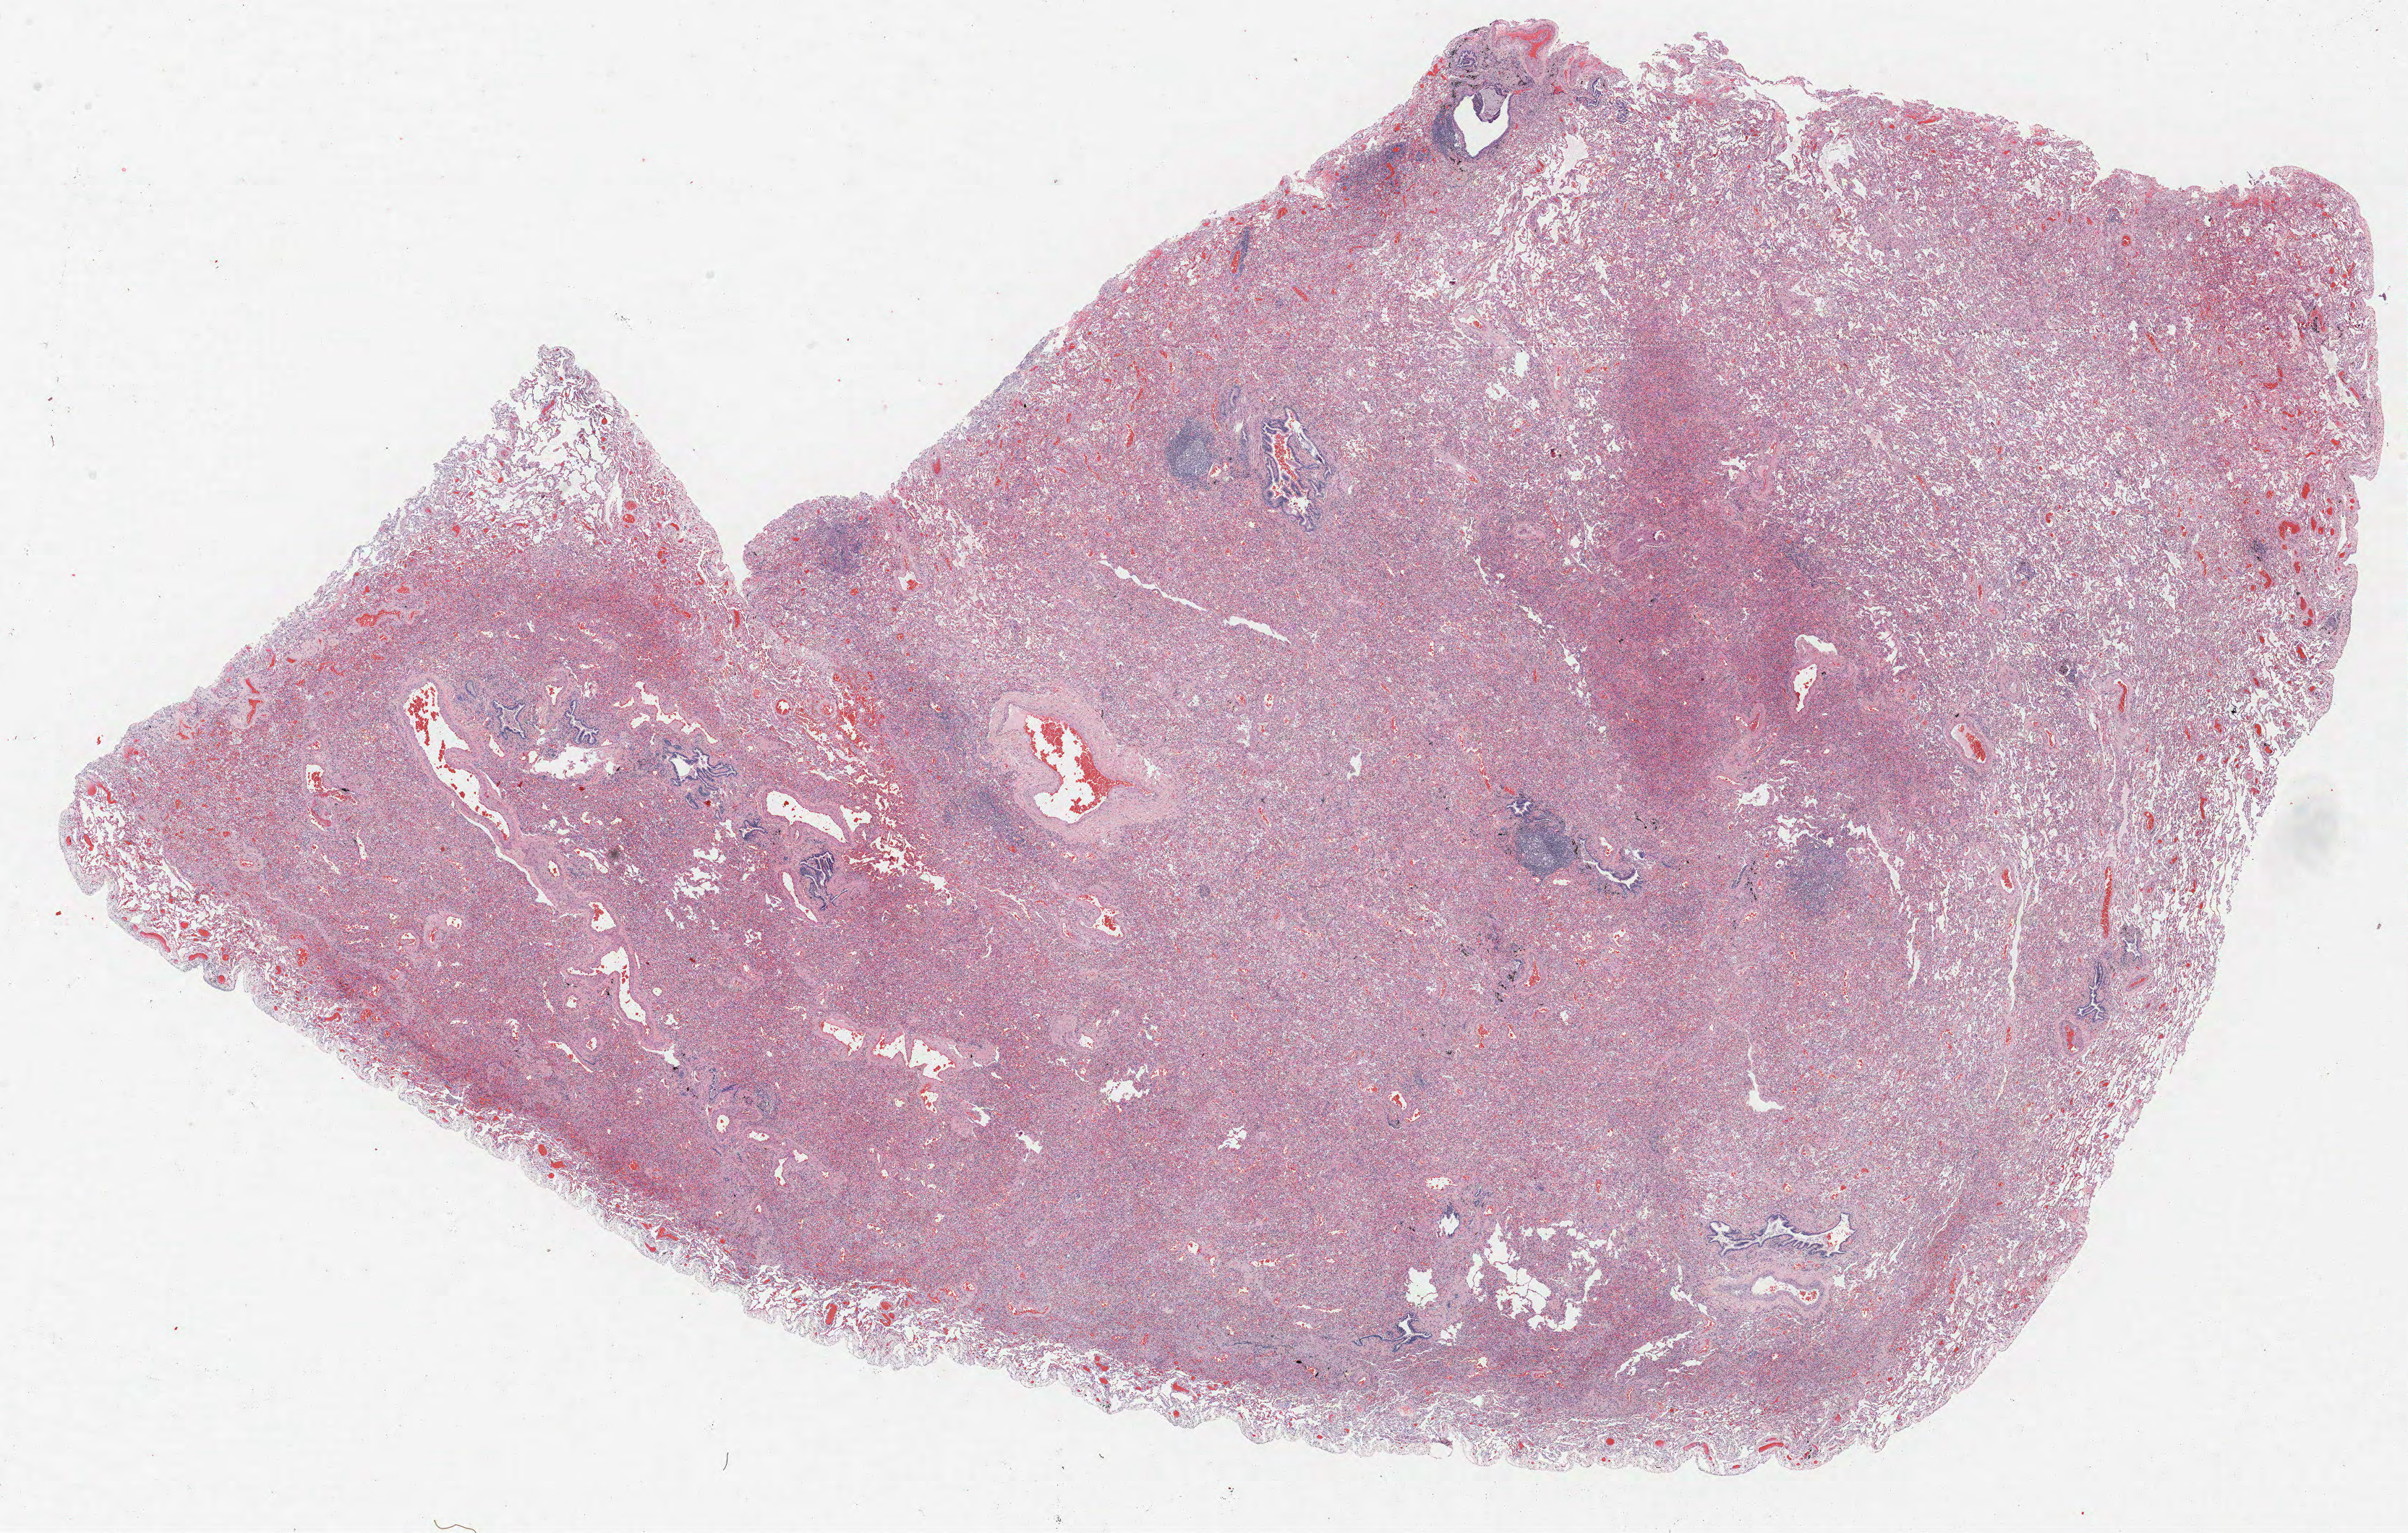
Whole-slide histology image, Hematoxylin and eosin (H&E) stained, a low-resolution overview of the entire scanned area, about 26.6 x 17.0 mm (from a 40x scan). Formalin-fixed paraffin-embedded (FFPE) section. Lung tissue. Female, age 65 at enrolment. Grade: moderately differentiated (G2).
- participant's lung-cancer diagnosis: Adenocarcinoma, NOS (ICD-O-3 8140/3)
- stage (AJCC 6th edition): IA
- ICD-O-3 topography: upper lobe of lung (C34.1)
- primary tumour location (clinical record): left upper lobe
- tumour size (pathology): 8 mm